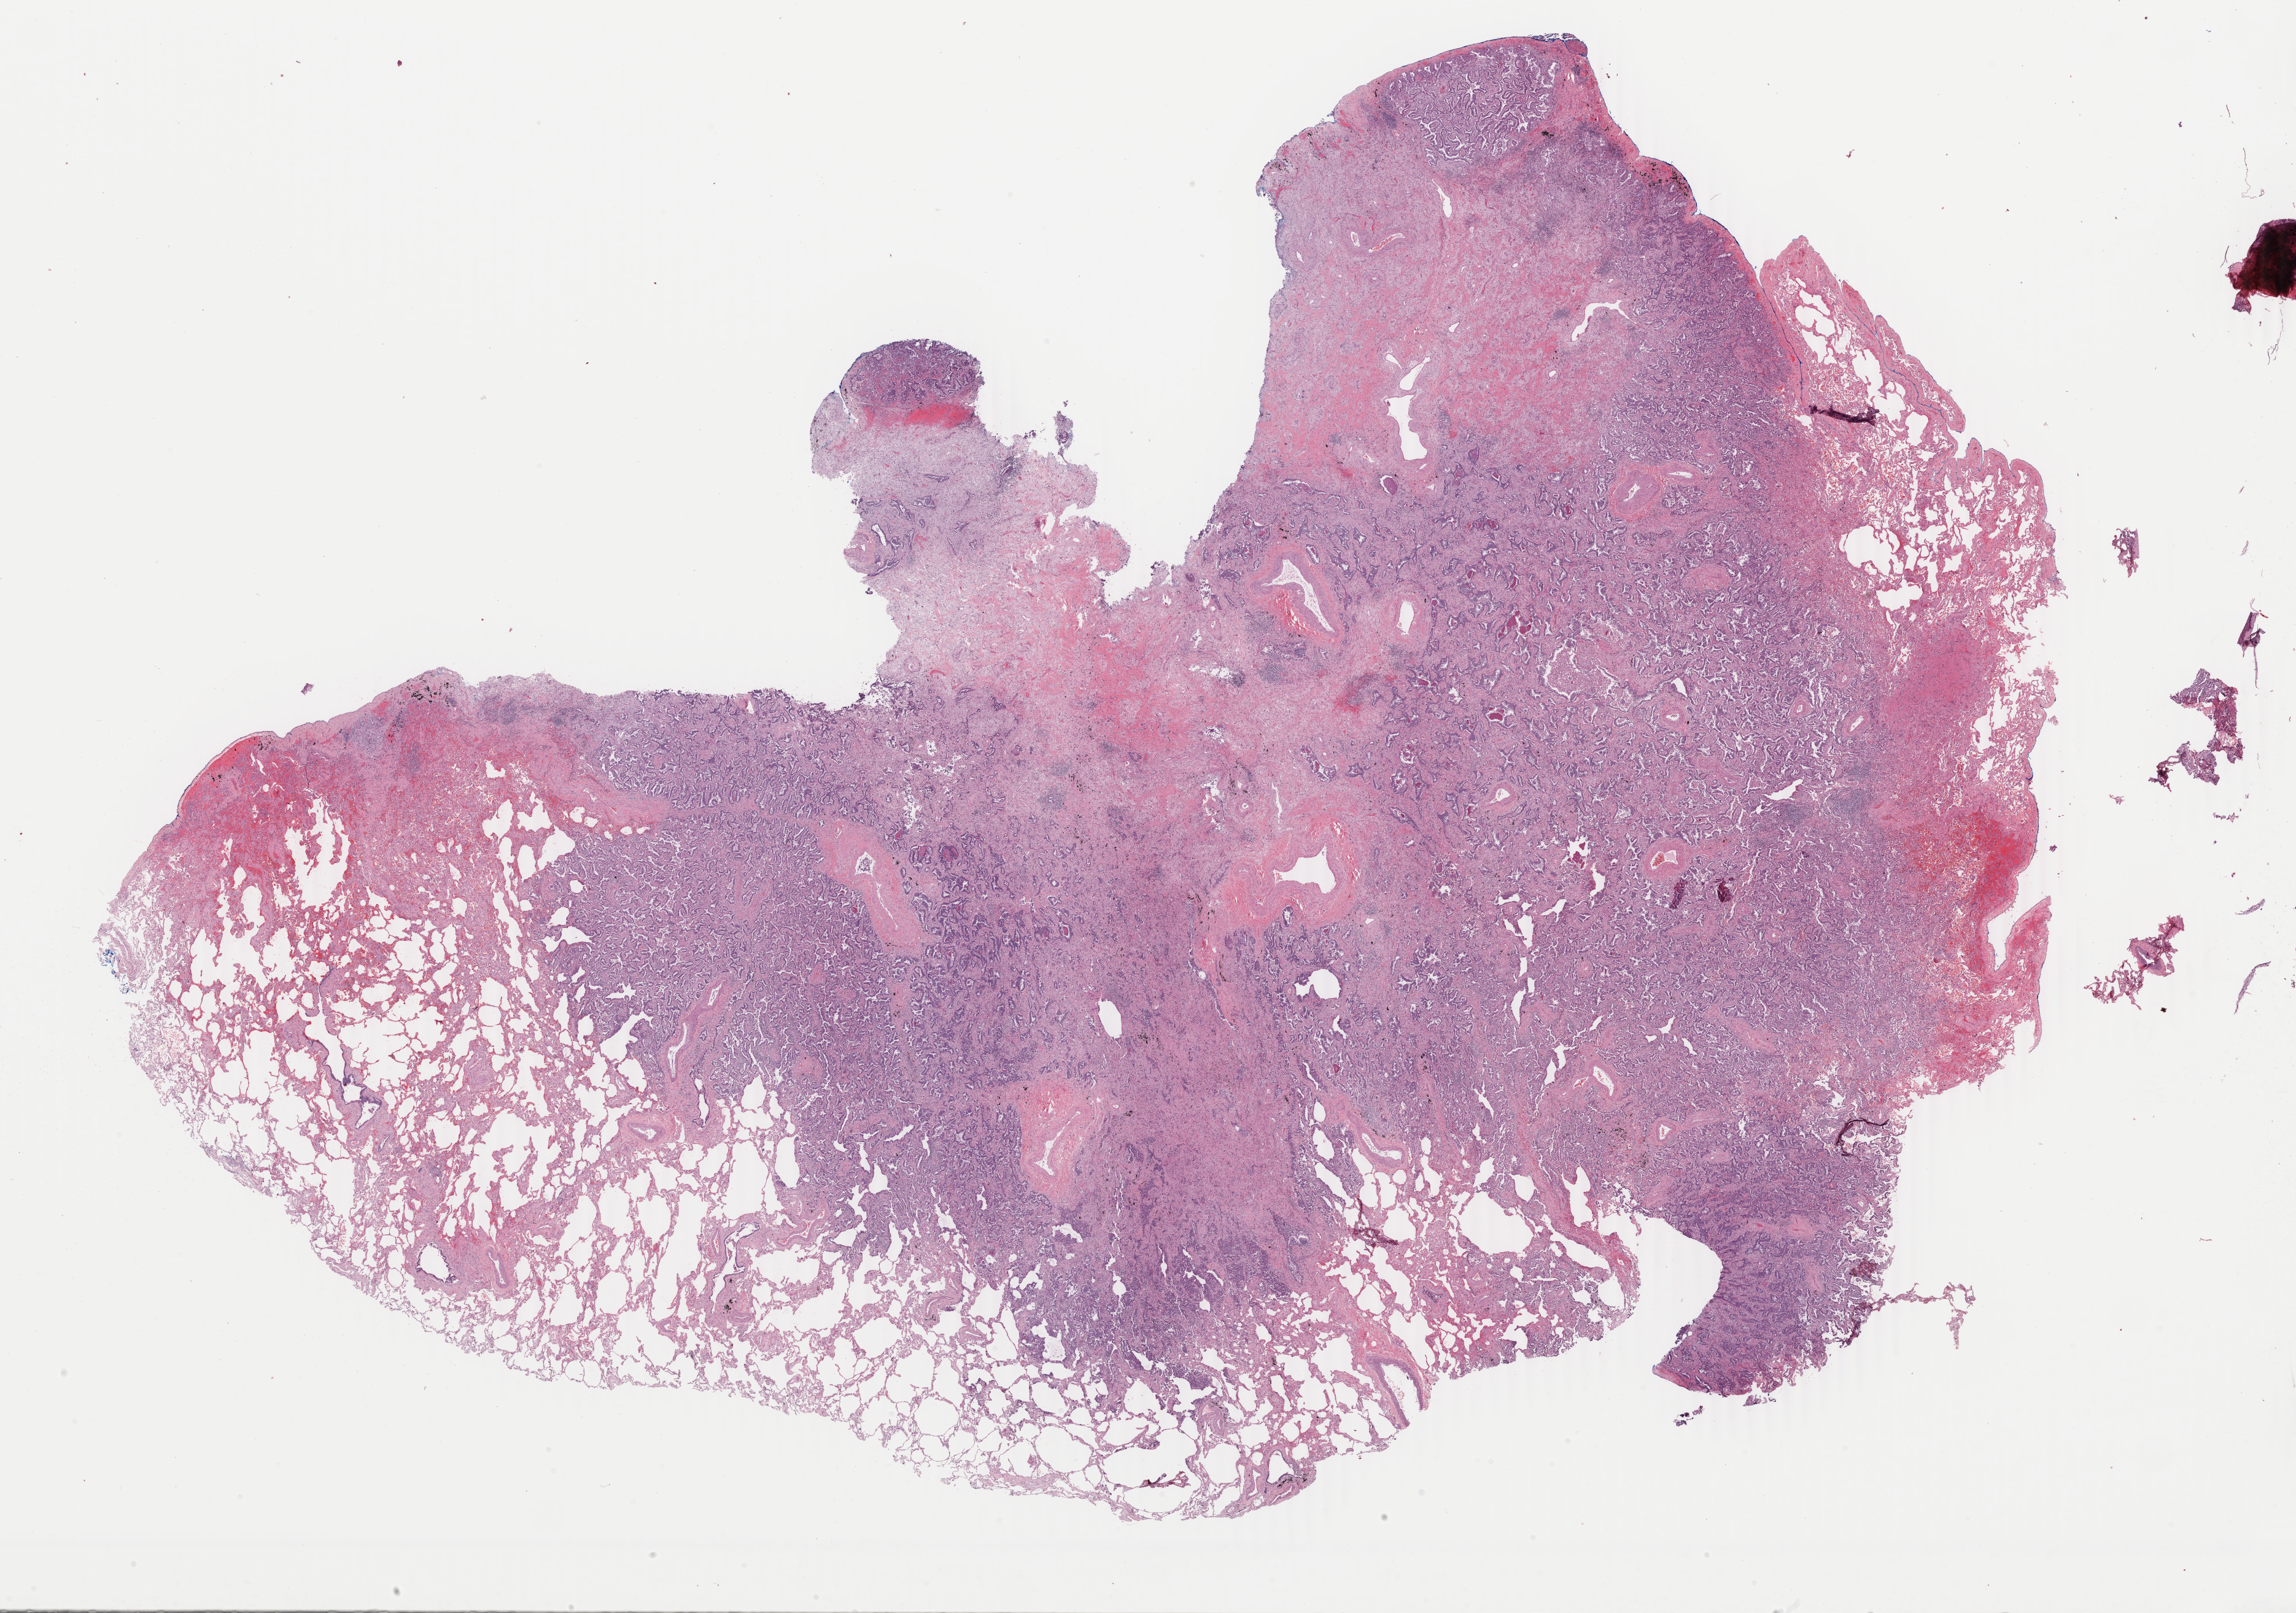
Whole-slide histology image, H&E — low-resolution overview of the scanned area, about 29.7 x 20.9 mm; formalin-fixed paraffin-embedded (FFPE) diagnostic section; lung, primary tumour sample. Female patient; age at initial diagnosis 63 years.
Pathologic diagnosis: Adenocarcinoma with mixed subtypes (upper lobe, lung).